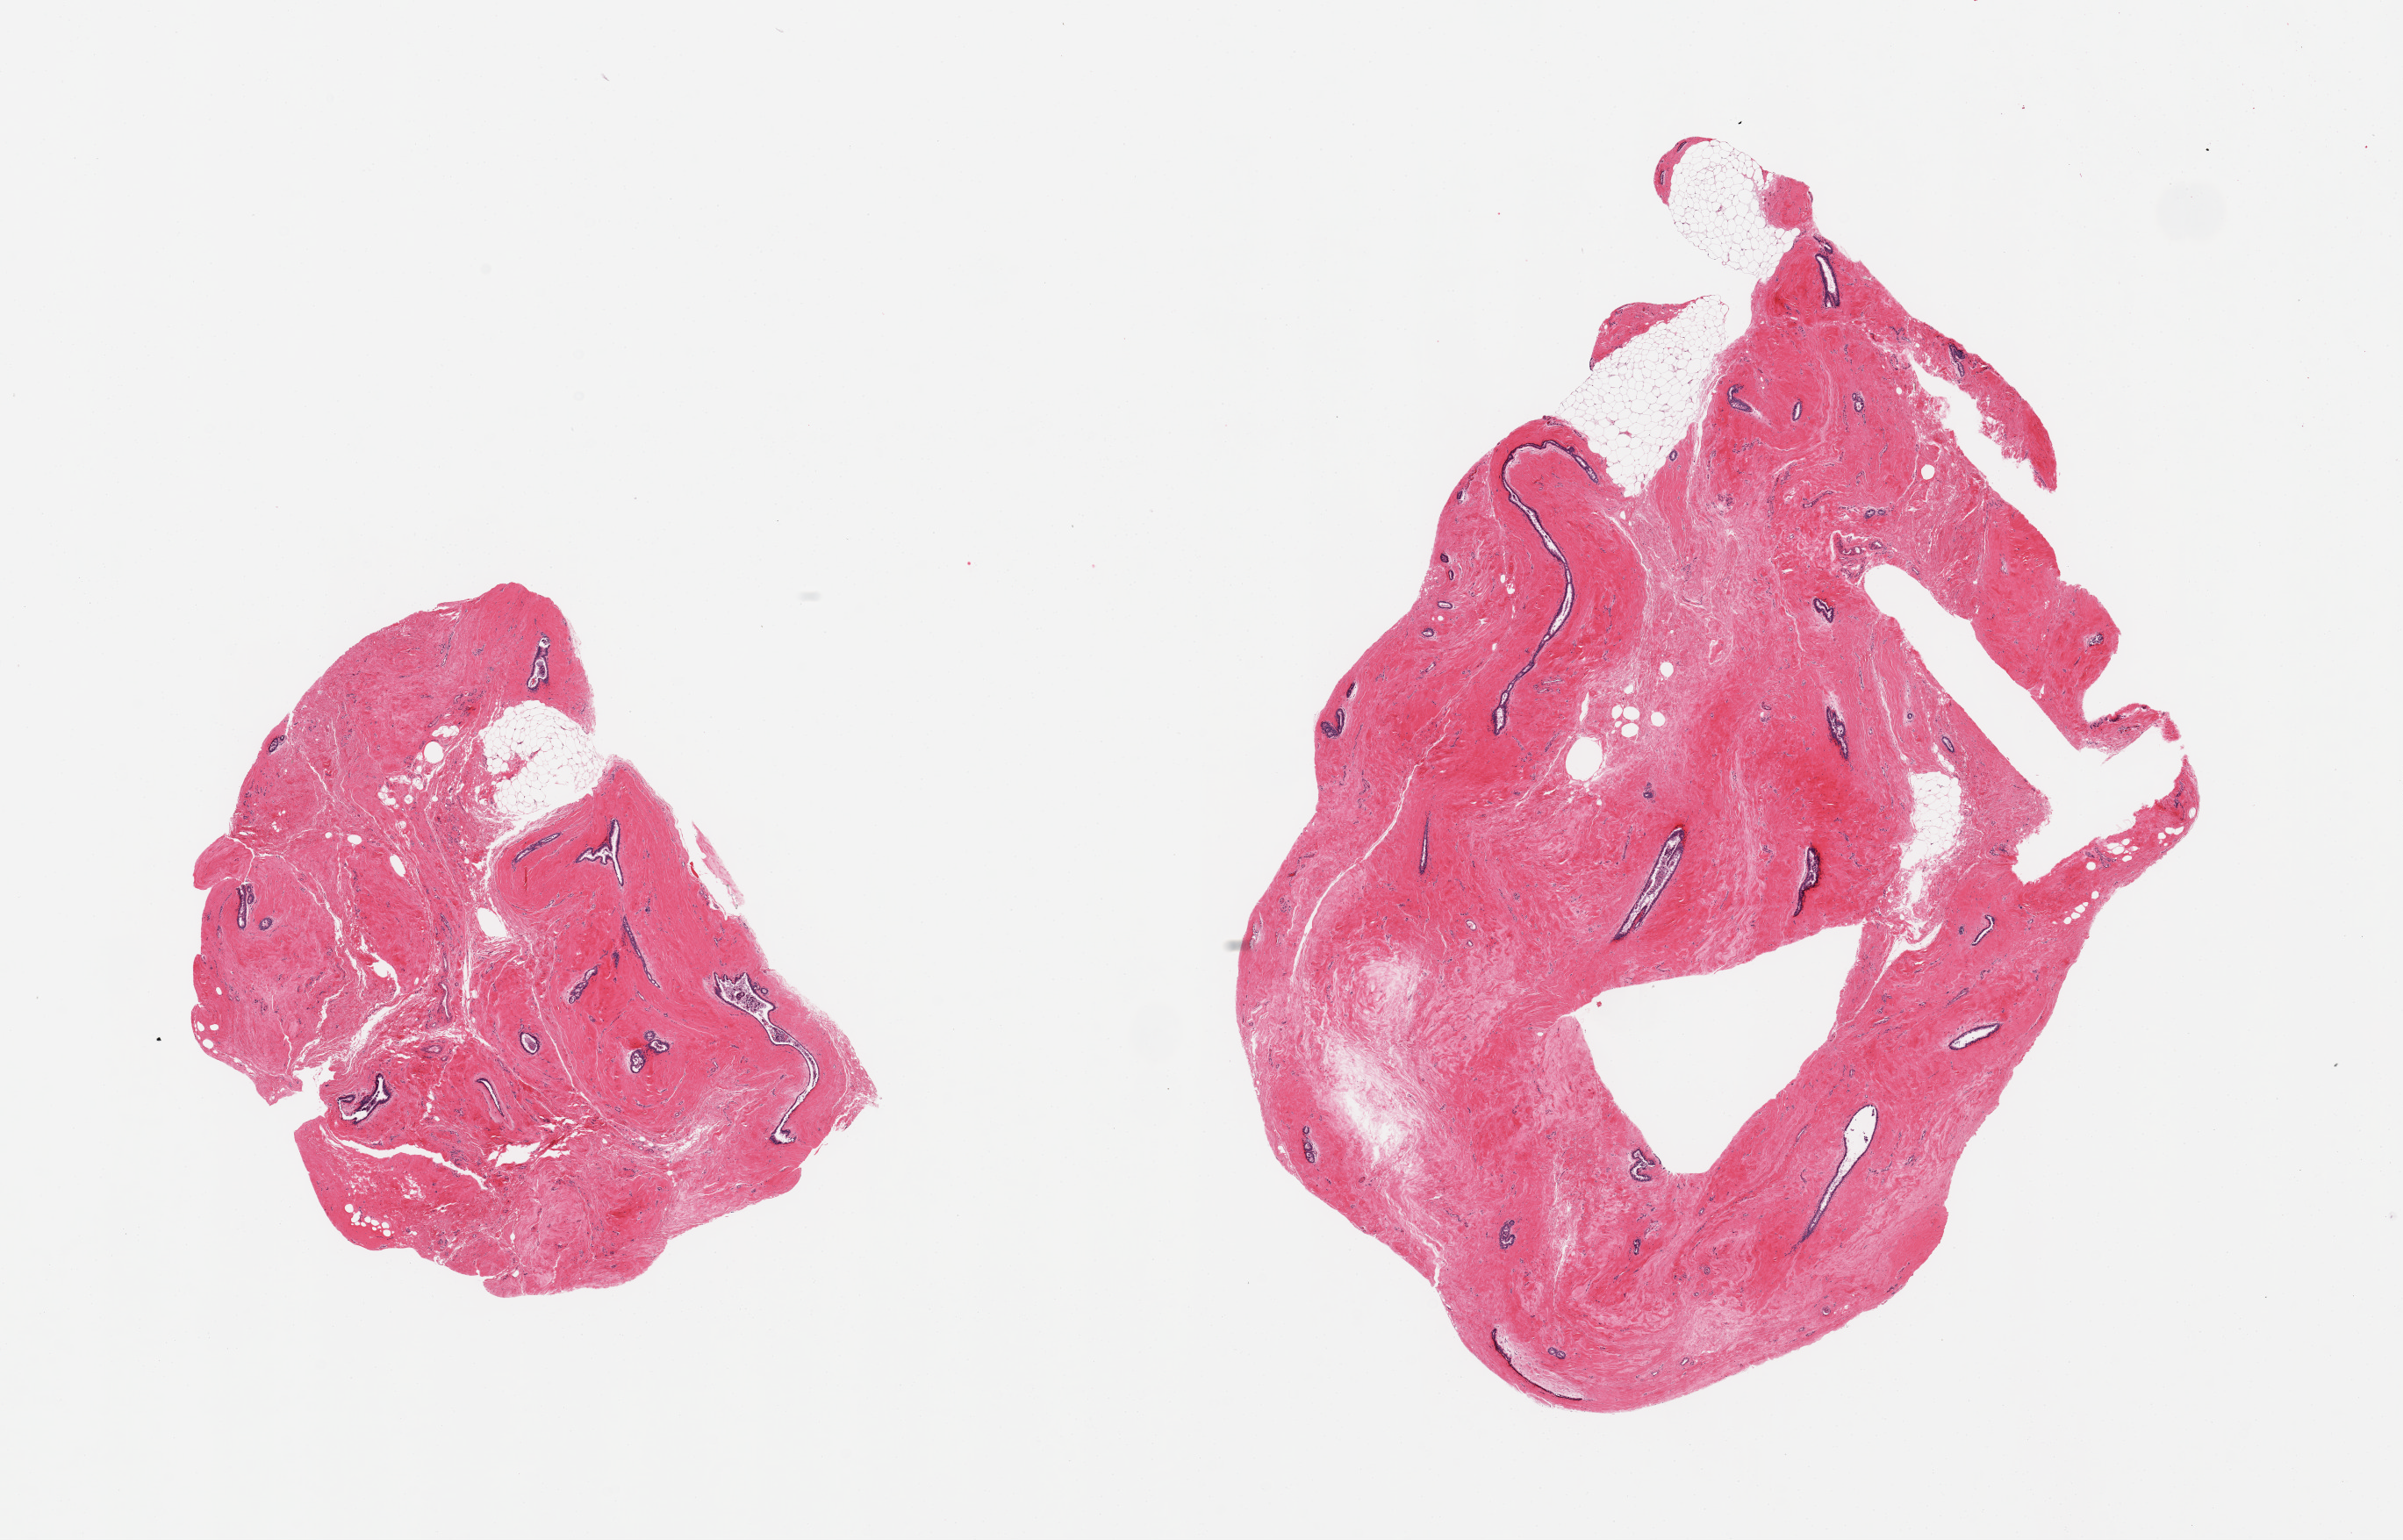
Whole-slide image, haematoxylin and eosin stain, low-resolution overview of the scanned area, about 21.7 x 13.9 mm (from a 20x scan). PAXgene-fixed, paraffin-embedded tissue. Sampled site (target tissue): breast. Donor tissue sample. Donor sex: male.
* pathologist's review note for this sample: 2 pieces; minimal fat with several ducts, some gynecomastoid features